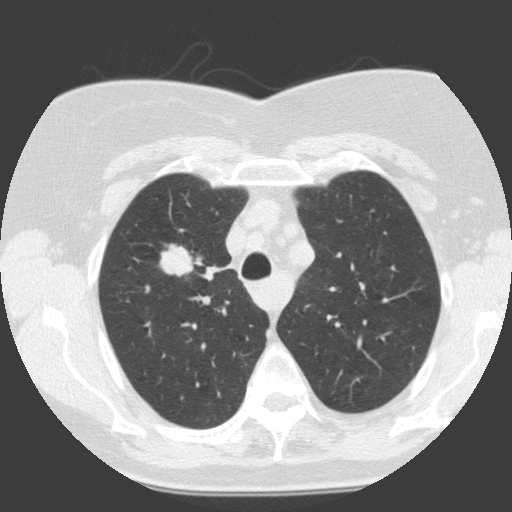
Low-dose screening chest CT, one axial slice. Slice 111 of 146 in the series (ordered by position). 120 kVp. Lung window (W 1500 / L -600 HU). 2 mm slice thickness. 512 × 512 image matrix.
Outlined on this slice (outlined manually by an expert reader):
- lesion 1 (tumor, upper lobe of right lung): bounding box [x1, y1, x2, y2] px = [159, 246, 194, 277]